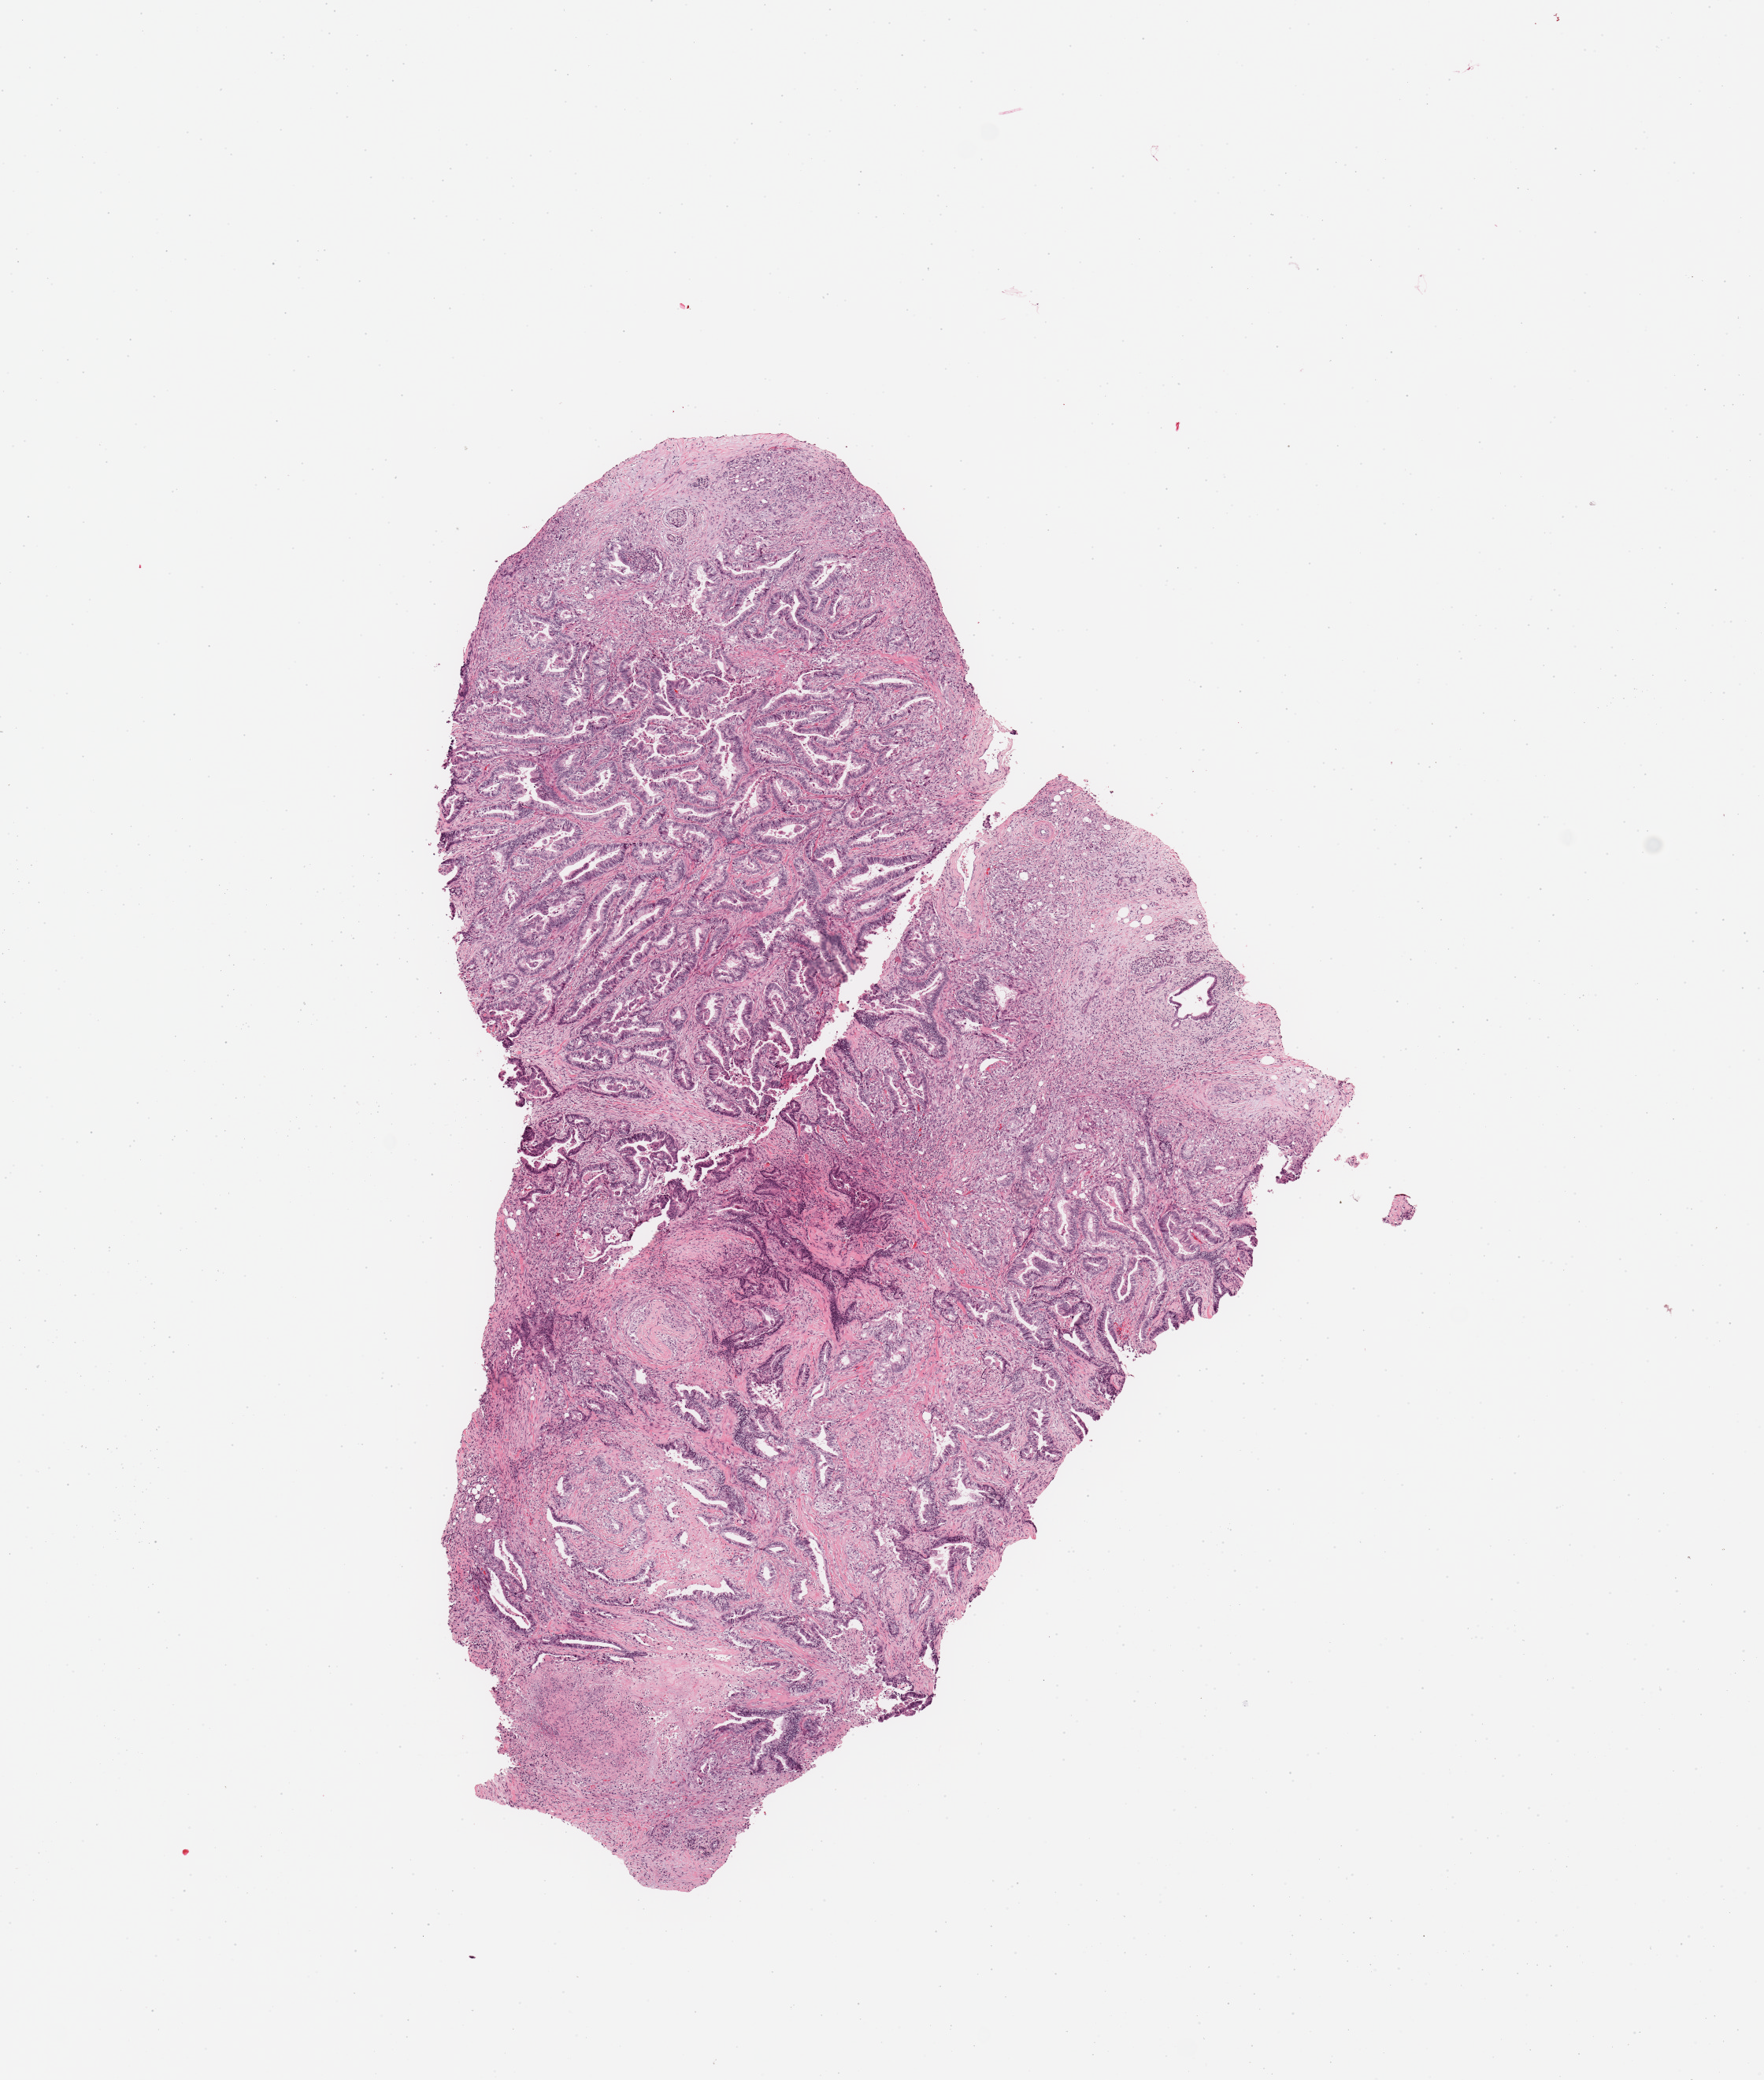
Digitized H&E tissue section (whole slide), a low-resolution overview of the entire scanned area, about 8.9 x 10.4 mm (slide scanned at 20x). Tumour tissue sample, sampled site: pancreas. 84-year-old female patient. Histologic grade: G1 (well differentiated). Composition of this section per pathologist review: tumour nuclei 75%, necrosis 10%.
Primary tumour site (as recorded): tail. Histologic diagnosis: Infiltrating duct carcinoma, NOS. AJCC pathologic stage: IIB.